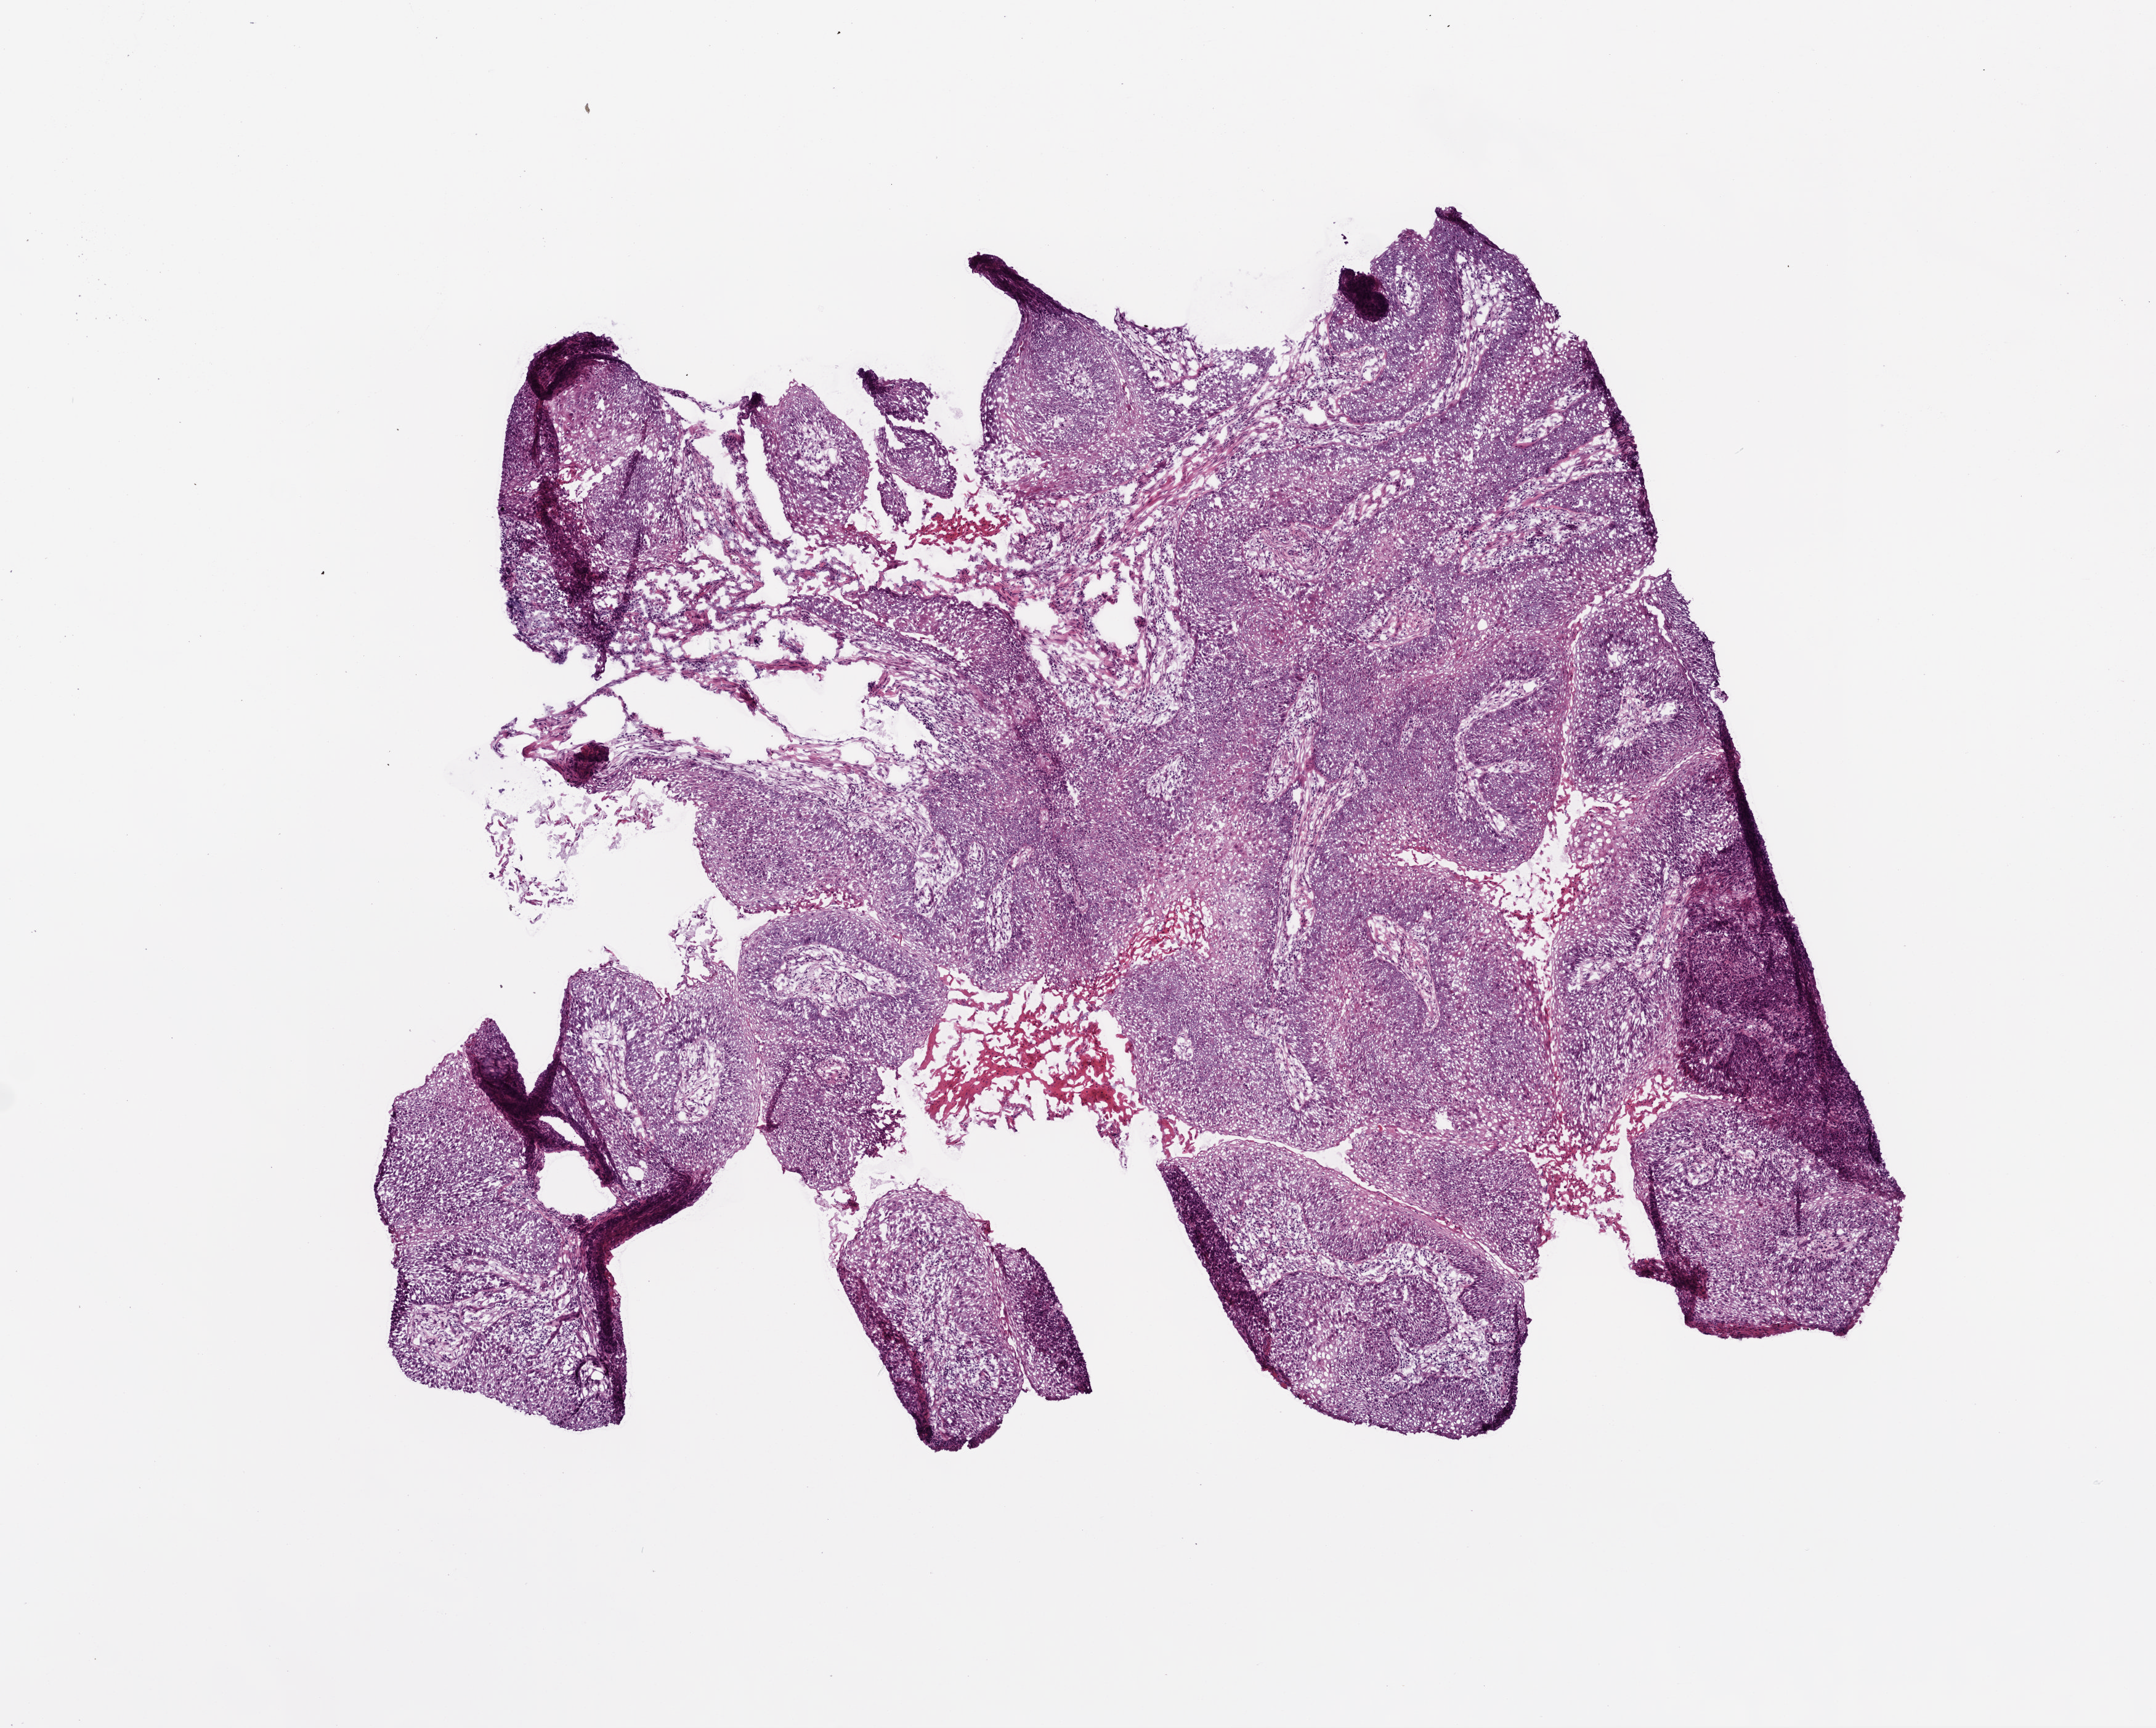
H&E-stained whole-slide image, shown as a low-resolution overview of the whole scanned area (about 7.0 x 5.6 mm); frozen section from the top of the tissue portion; head and neck, primary tumour sample. Patient: male, age at initial diagnosis 59 years. Histologic grade: G2 (moderately differentiated). Pathologist review of this section (percent, as recorded): tumour cells 90%, tumour nuclei 82%, normal cells 0%, stromal cells 5%, necrosis 5%. Inflammatory infiltration, as recorded: lymphocyte infiltration 10%, neutrophil infiltration 1%.
Lymph nodes positive (case pathology): 0 of 24 examined. AJCC pathologic stage: III (6th edition). Pathologic diagnosis: Squamous cell carcinoma, NOS (overlapping lesion of lip, oral cavity and pharynx).